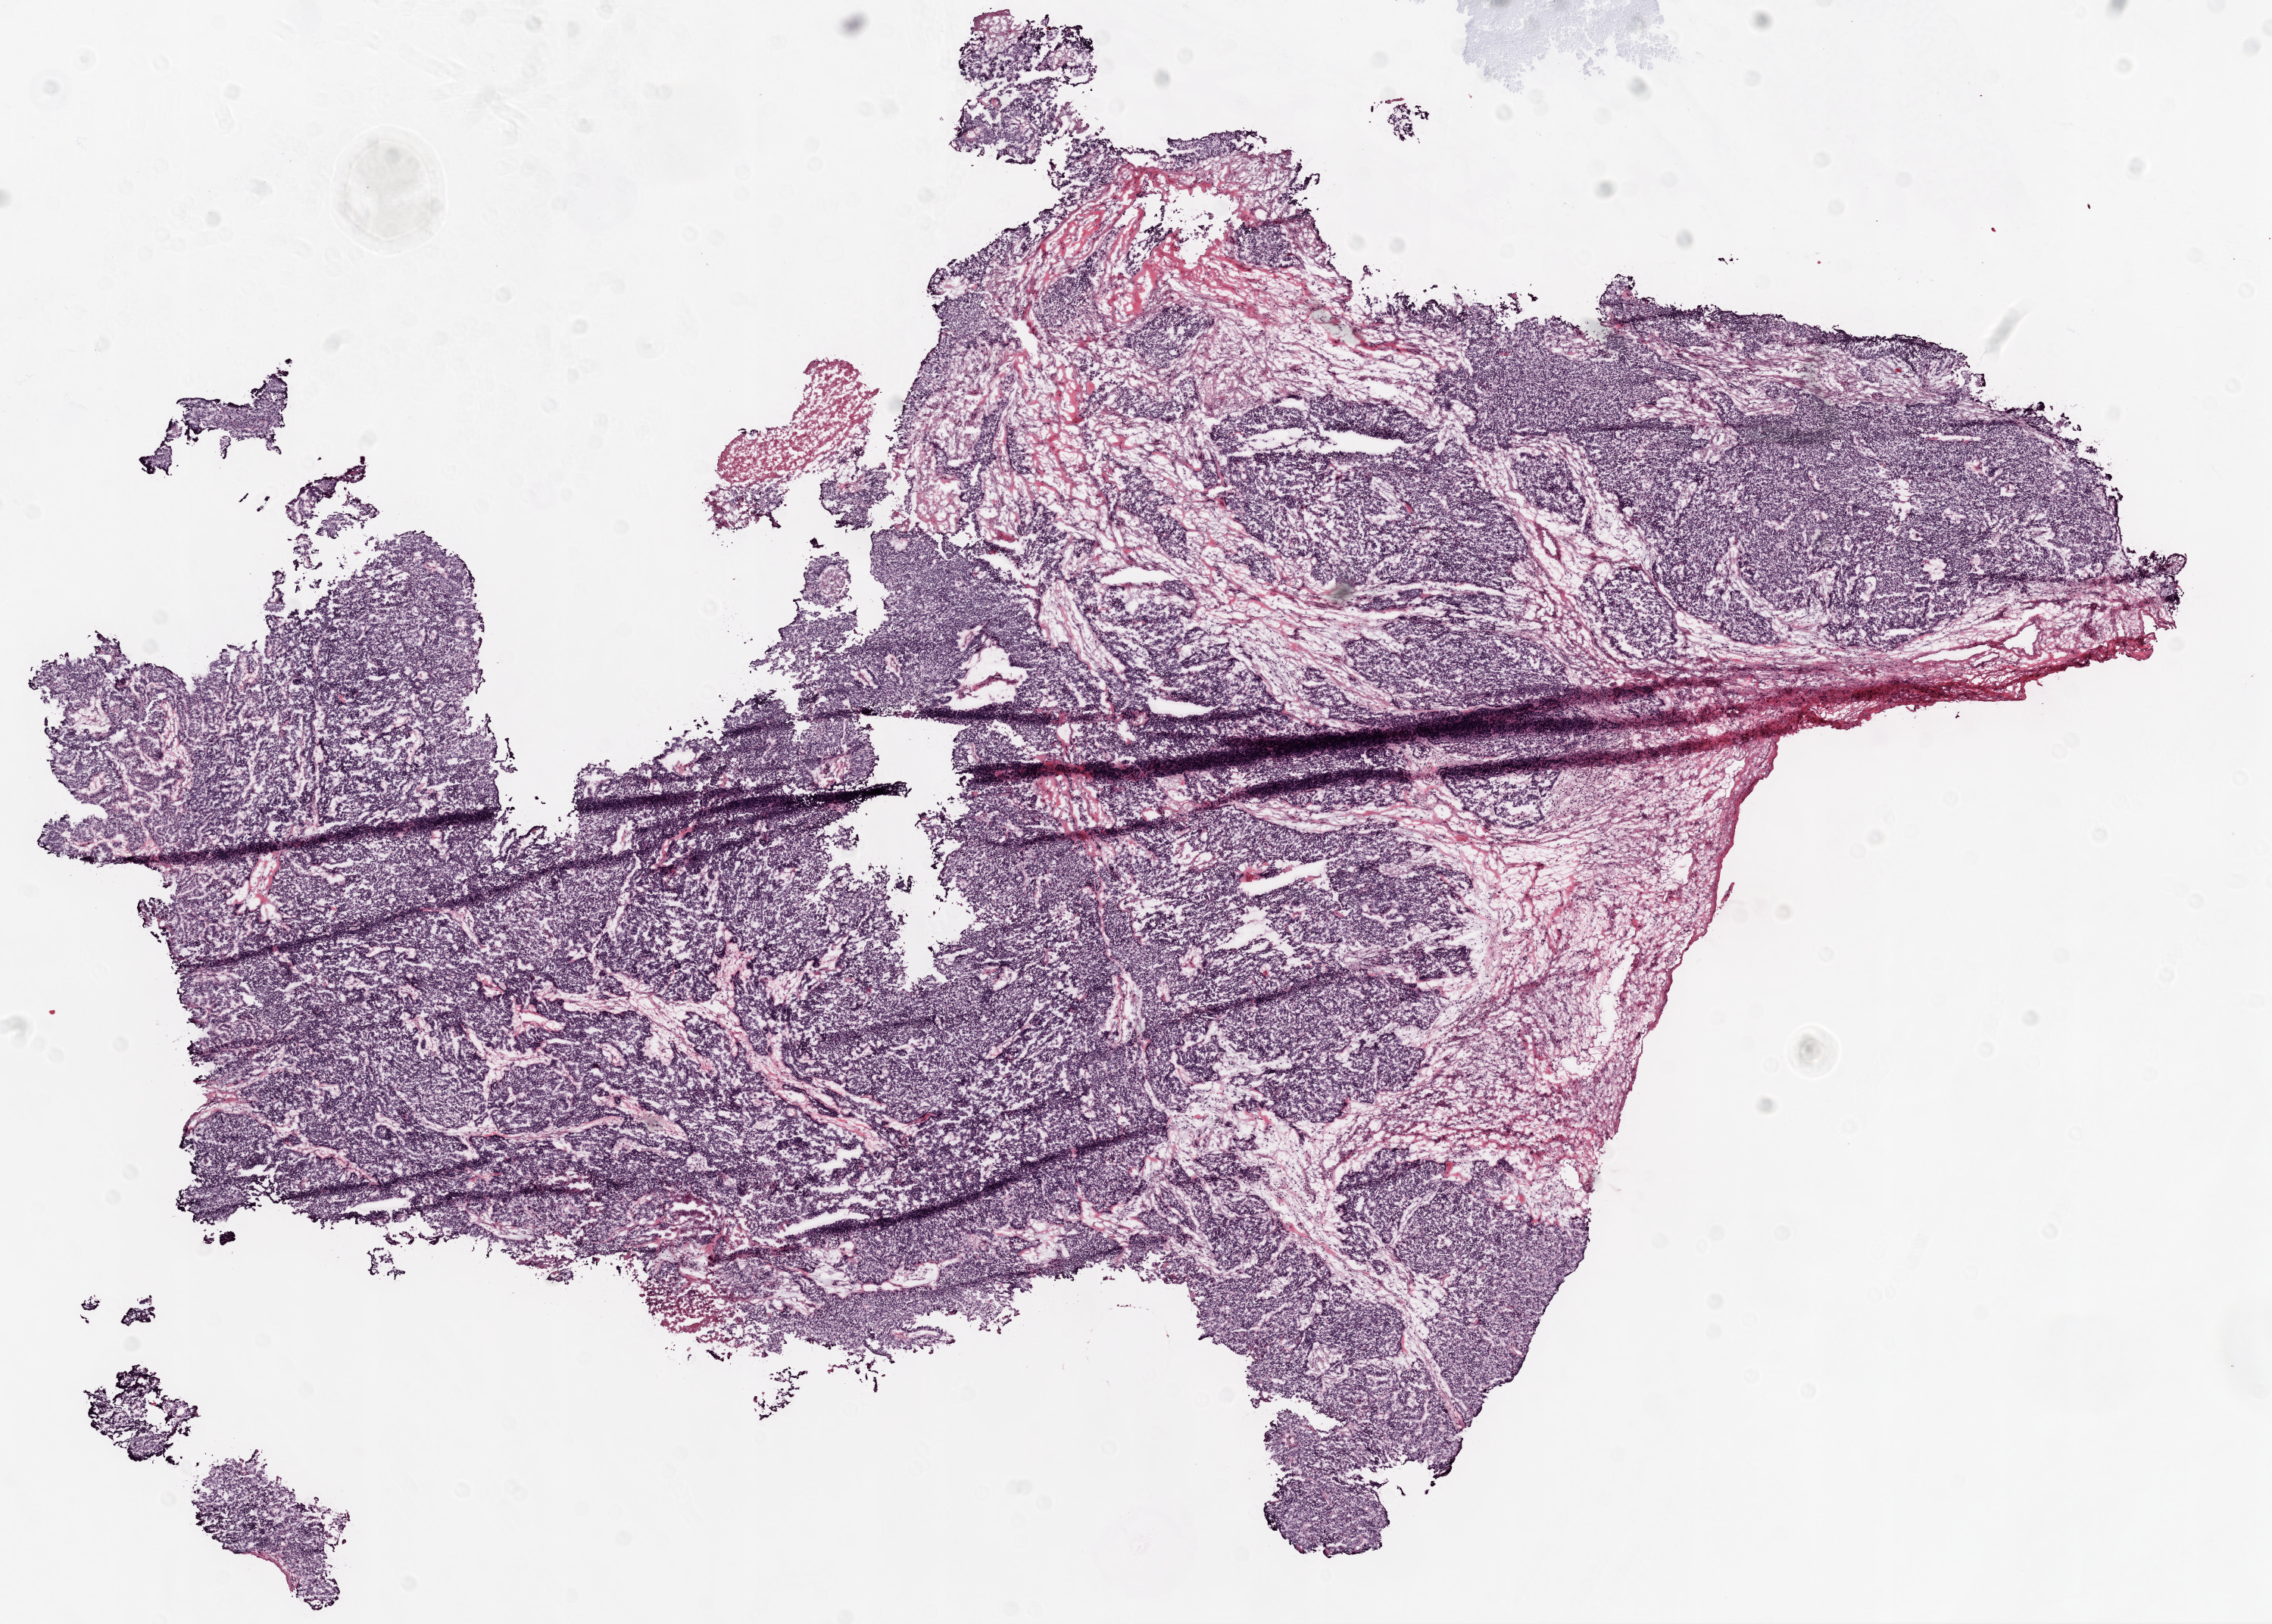
Digitized H&E-stained tissue section (whole slide), whole scanned area (about 12.0 x 8.6 mm, slide scanned at 20x) shown as a low-resolution overview. Frozen section from the top of the tissue portion. Primary tumour sample from the ovary. Patient: female, age at initial diagnosis 56 years. Histologic grade: G2 (moderately differentiated). Slide review estimates, as recorded: tumour cells 90%, tumour nuclei 95%, normal cells 0%, stromal cells 0%, necrosis 10%.
• laterality: bilateral
• FIGO stage: IIIC
• diagnosis: Serous cystadenocarcinoma, NOS